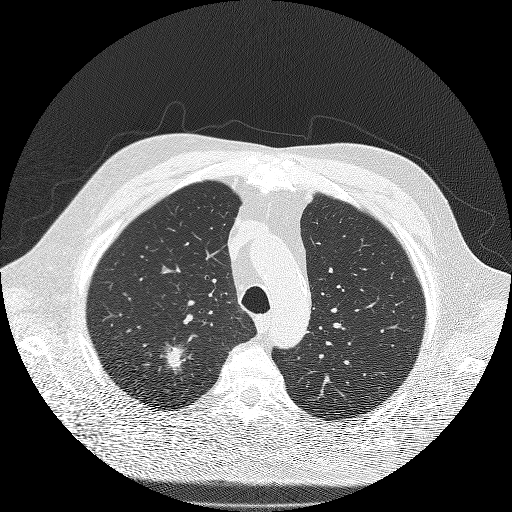
Low-dose screening chest CT, axial slice, second screening round (one year after baseline), lung window (W 1500 / L -600 HU), 2 mm slice thickness, 120 kVp, 512 × 512 image matrix. Male participant, aged 71 years at enrolment.
• Expert-annotated lung lesion, bounding box (x1, y1, x2, y2) in pixels: (139, 328, 202, 390).
• The screening reader recorded 3 non-calcified nodules or masses ≥4 mm on this exam (right upper lobe, right upper lobe, right lower lobe); which of them this box marks is not recorded.
• Later outcome: lung cancer diagnosed 59 days after this screen — bronchiolo-alveolar adenocarcinoma, NOS, right upper lobe, moderately differentiated (G2), stage IIIA (AJCC 6th edition), 25 mm at pathology.